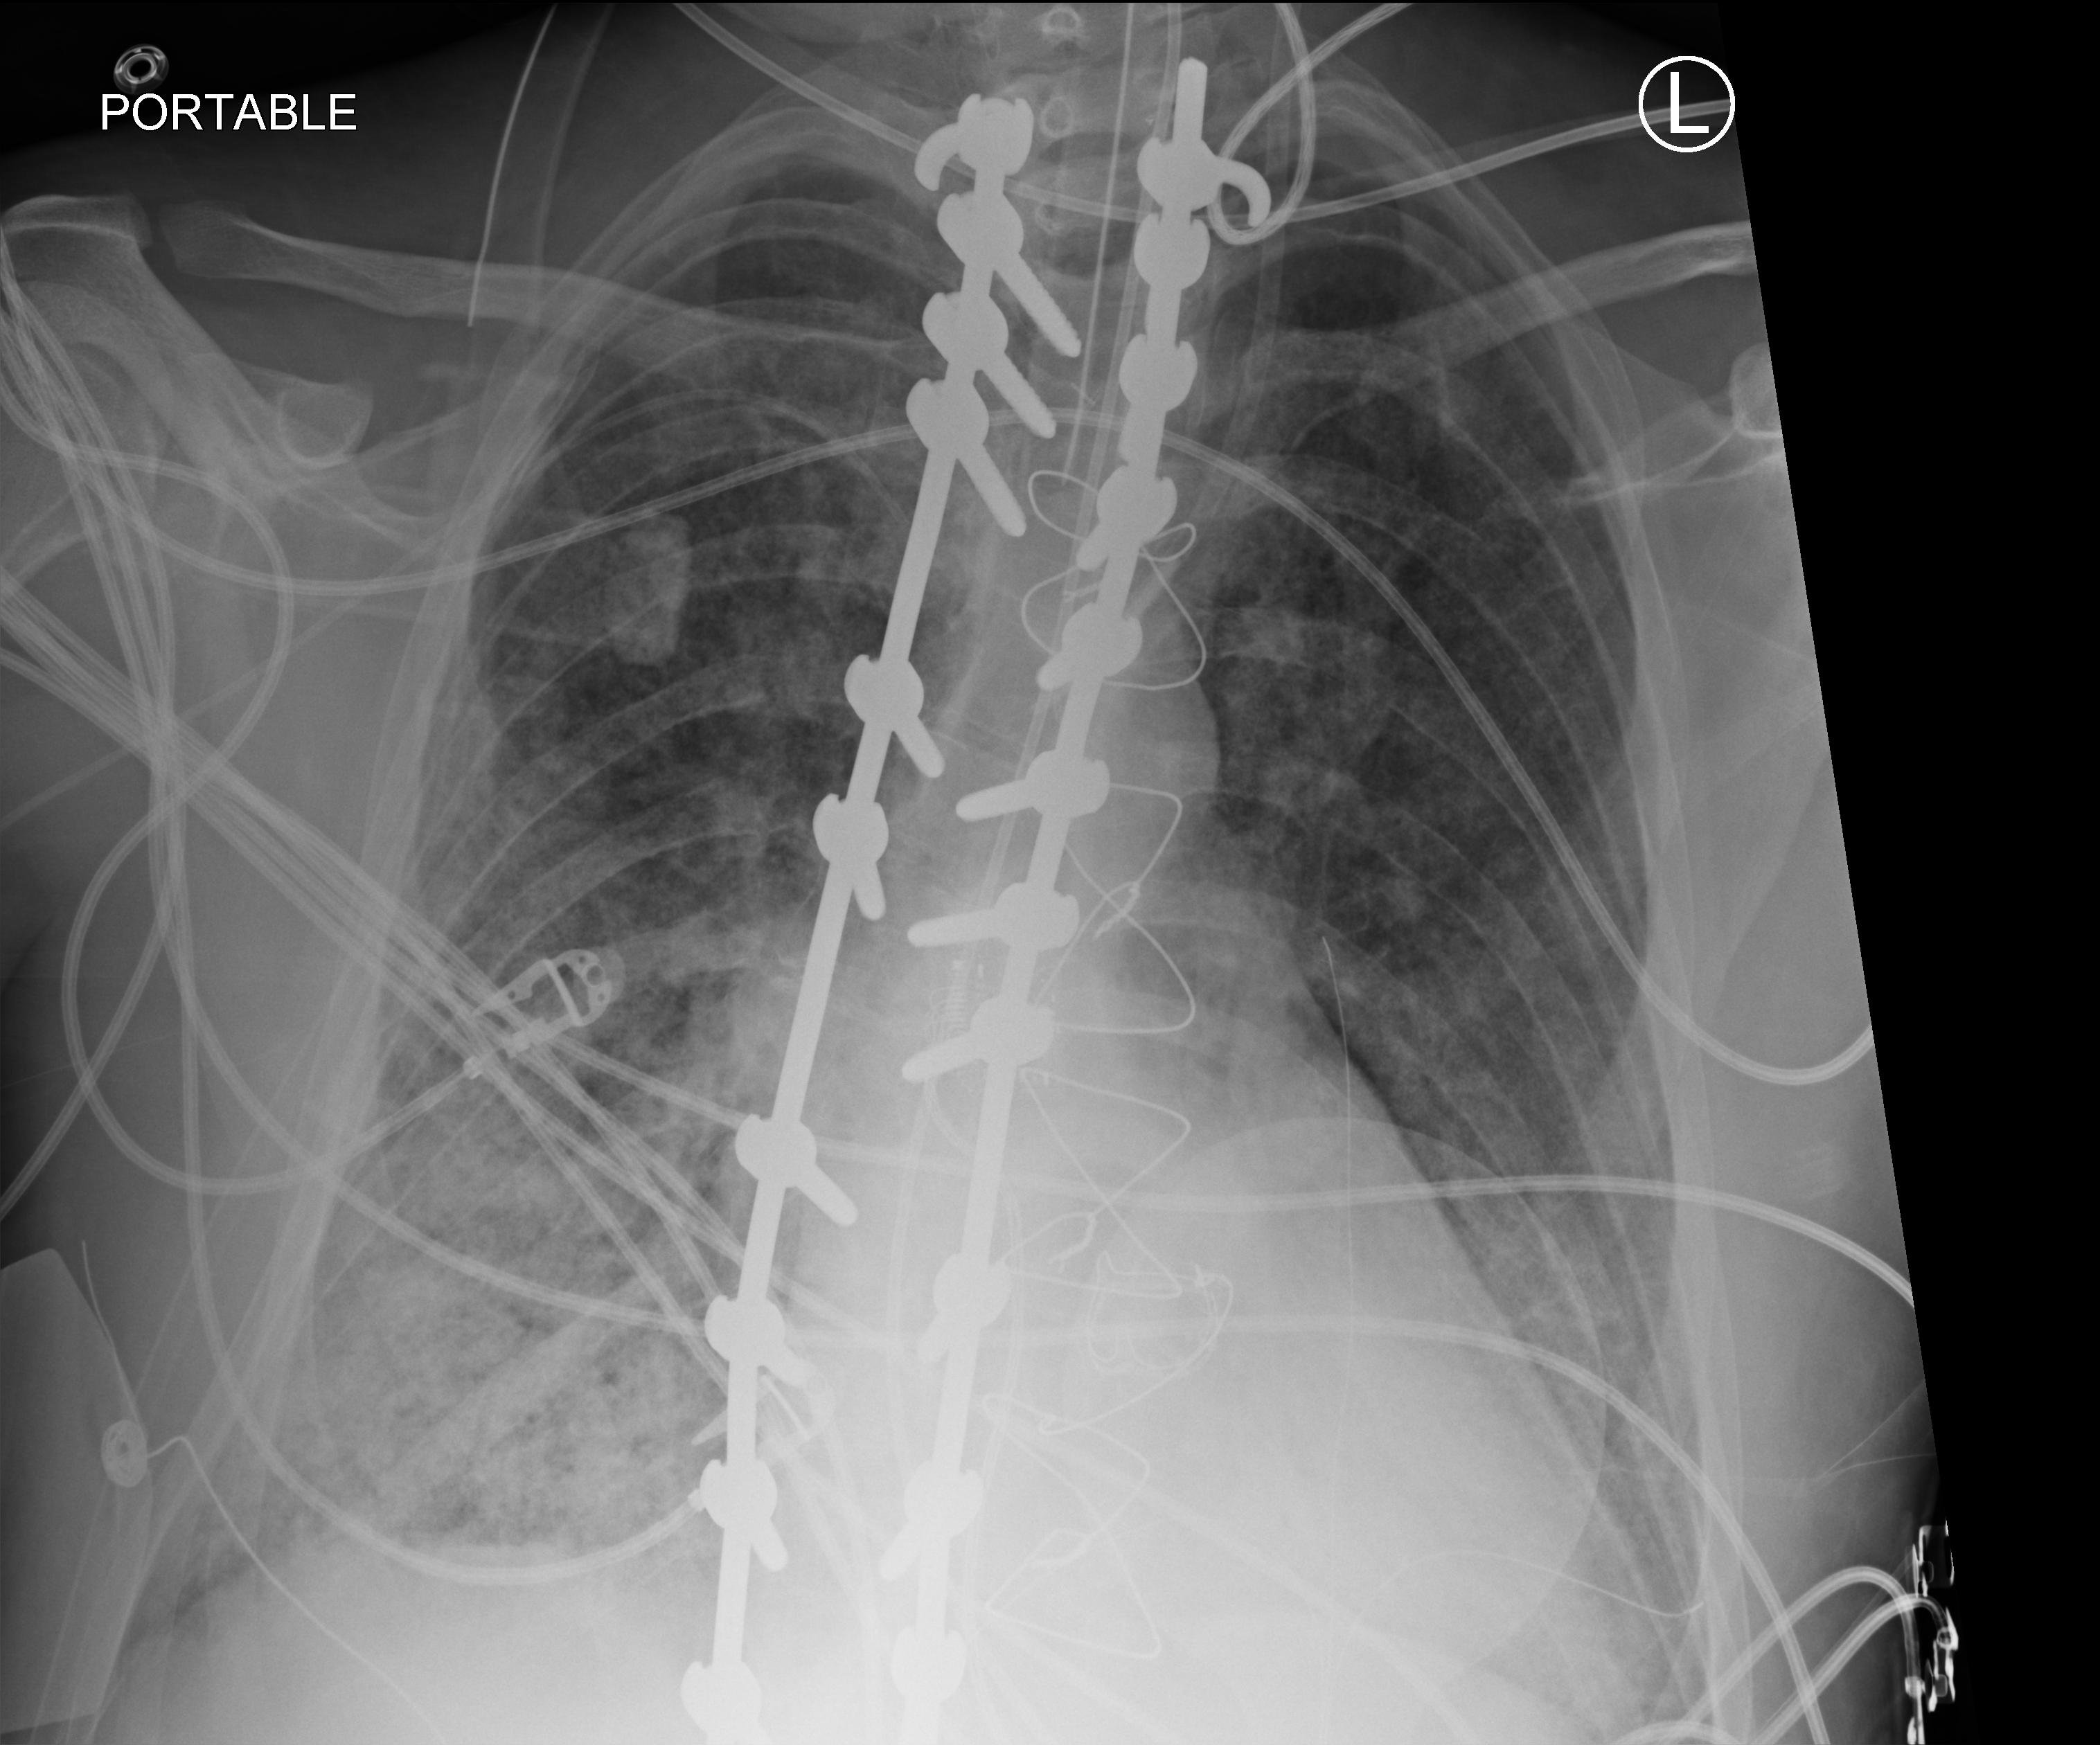
Bedside chest radiograph (computed radiography); anteroposterior (AP) projection. Patient hospitalised with COVID-19, aged 18–59 years.
From the hospital-stay record, not from the radiograph (when in the stay this image was taken is not recorded): admitted to intensive care during this hospital stay: yes.